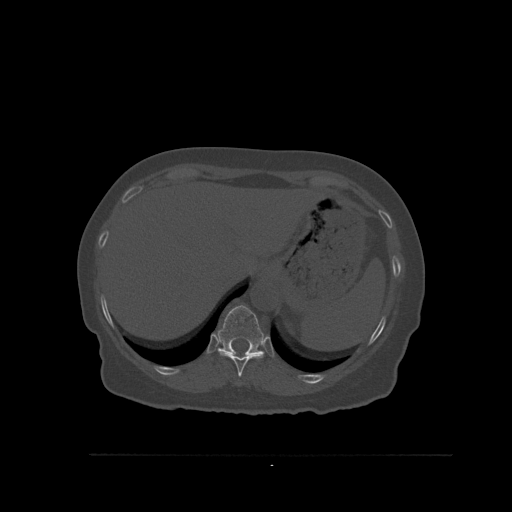
CT including the spine, one axial slice. Position 311 of 527 along the scan axis. Bone window (W 1800 / L 400 HU). 1.5 mm slice thickness. 512 × 512 image matrix, field of view 470 × 470 mm. Female patient, age 73 years. Case-level facts recorded for this patient, not image findings: primary cancer: breast; vertebrae with lytic lesions (as recorded): L2.
Structures marked on this image (semi-automatic segmentation, software-assisted and operator-edited):
- T10 vertebra: box from (x=217, y=348) to (x=264, y=377) px
- T11 vertebra: (x=217, y=305)–(x=264, y=356)